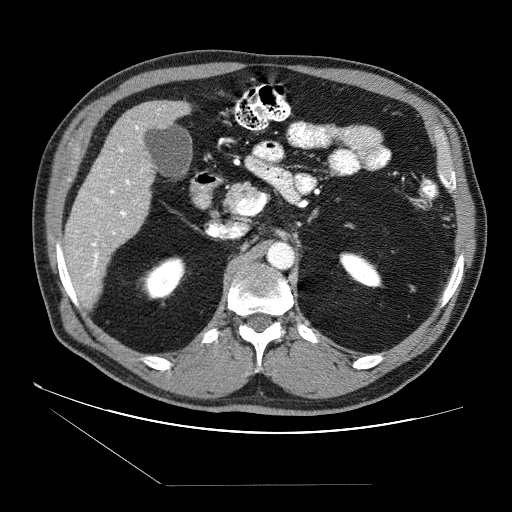
Contrast-enhanced abdominal CT (liver protocol), one axial slice. Reconstruction kernel STANDARD. 120 kVp. Soft-tissue window (W 400 / L 40 HU). 2.5 mm slice thickness. 512 × 512 image matrix, field of view 400 × 400 mm. From the clinical record (not read from this slice): diagnosis: hepatocellular carcinoma (patient treated with transarterial chemoembolisation; whether this scan precedes or follows treatment is not stated here); TNM stage (as recorded): Stage-II; Child-Pugh class: B; tumour differentiation: no biopsy; tumour nodularity: multinodular.
Structures marked on this image (semi-automatic segmentation, software-assisted and operator-edited):
- liver parenchyma outside the tumour (the mass and vessels are separate outlines, so this box may not span the whole liver): bounding box (x1, y1, x2, y2) in pixels: (64, 100, 190, 294)
- liver vessels: (76, 109, 160, 278)